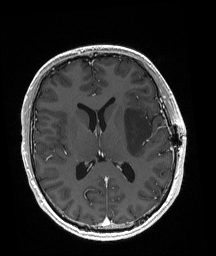
Brain MRI from a brain-tumour surgery series, one axial slice; slice 92 of 192 in the series (ordered by position); T1-weighted post-contrast; 1 mm slice thickness; 216 × 256 image matrix. From the clinical record (not read from this slice): histopathology: Astrocytoma; WHO grade: 3.
Annotated regions visible in this slice (expert manual segmentation):
- tumour: bounding box [x1, y1, x2, y2] px = [124, 109, 152, 157]